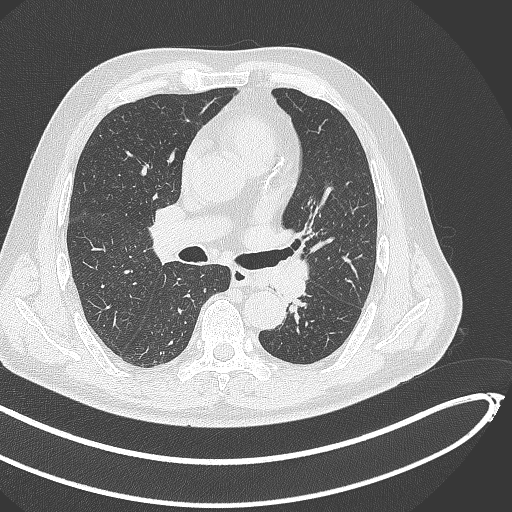
Chest CT, one axial slice; position 266 of 468 along the scan axis; lung window (W 1500 / L -600 HU); 1 mm slice thickness; 512 × 512 image matrix, field of view 400 × 400 mm. Male patient, age 64 years. Case-level facts recorded for this patient, not image findings: clinical TNM (as recorded): T1c N0 M0; histopathological grade: G2.
Annotated regions visible in this slice (rectangle marked by the reading radiologist):
- lung tumour (recorded histology: squamous cell carcinoma): bounding box <266,254,312,308> (left, top, right, bottom; pixels)